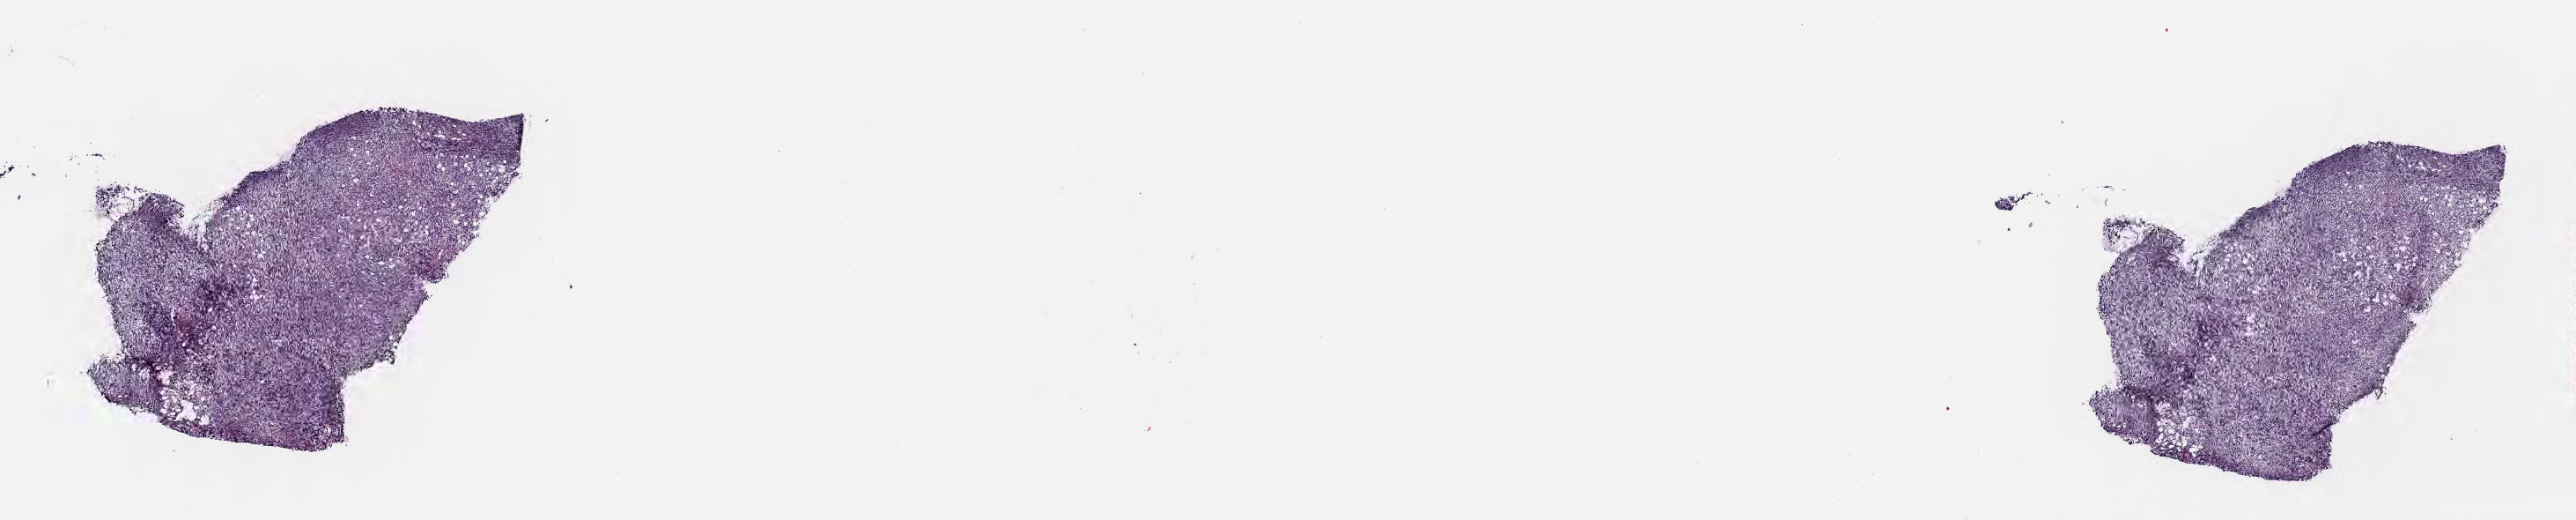
Whole-slide image, H&E stain, low-resolution overview of the scanned area, about 23.6 x 4.8 mm, cryosection, primary tumor, anatomic site: retroperitoneum. Male patient; age at initial diagnosis 7 years. Slide review estimates, as recorded: tumor cells 90%, tumor nuclei 90%, stromal cells 5%, necrosis 0%, normal cells 5%. Infiltration values recorded for this section: lymphocyte infiltration 80%, monocyte infiltration 15%, neutrophil infiltration 0%.
Histologic diagnosis: Diffuse large B-cell lymphoma, NOS. Ann Arbor stage (patient): Stage IV.